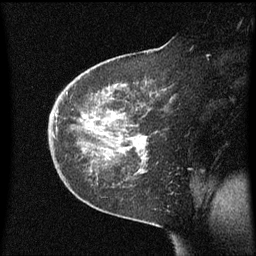
Breast MRI (dynamic contrast-enhanced), one sagittal slice; slice 39 of 60 in the series (ordered by position); dynamic contrast-enhanced series, image 2 of 3 at this slice position (ordered by acquisition); 1.5 T; TE 4.2 ms, TR 8.4 ms; 256 × 256 image matrix. Patient: female, 38 years. From the clinical record (not read from this slice): setting: breast cancer imaged before/during neoadjuvant chemotherapy; receptor status: HER2-positive.
Structures marked on this image (semi-automatic segmentation, software-assisted and operator-edited):
- analysis volume of interest (the breast-tissue region the enhancement analysis was run in; not a lesion): bounding box <49,50,175,185> (left, top, right, bottom; pixels)
- tumour enhancement mask (voxels above the 70 % enhancement threshold inside the analysis volume of interest): <136,140,140,141>